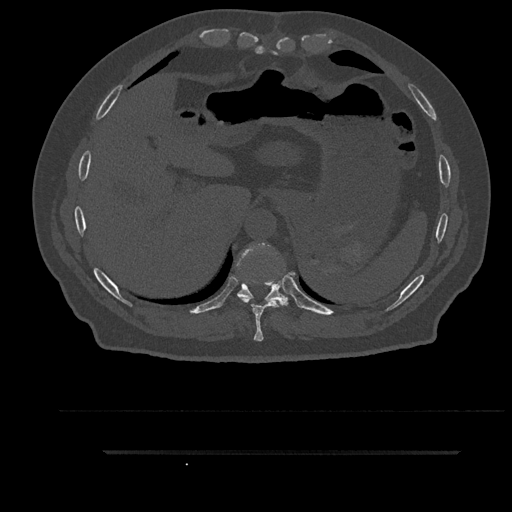
CT including the spine, one axial slice; position 394 of 797 along the scan axis; reconstruction kernel Br40s/3; bone window (W 1800 / L 400 HU); 512 × 512 image matrix, field of view 432 × 432 mm. Patient: male, 63 years. From the clinical record (not read from this slice): primary cancer: renal; vertebrae with lytic lesions (as recorded): T8.
Outlined on this slice (semi-automatically segmented with operator editing):
- T10 vertebra: bounding box [x1, y1, x2, y2] px = [236, 243, 288, 307]
- T9 vertebra: [237, 244, 288, 342]